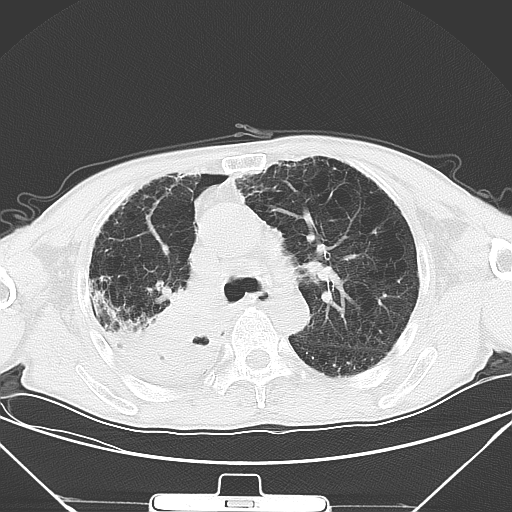
Chest CT, one axial slice; position 32 of 50 along the scan axis; 120 kVp; lung window (W 1500 / L -600 HU); 5 mm slice thickness; 512 × 512 image matrix, field of view 373 × 373 mm. Patient: male, 65 years. Case-level facts recorded for this patient, not image findings: clinical TNM (as recorded): T3 N1 M1a.
Structures marked on this image (rectangle marked by the reading radiologist):
- lung tumour (recorded histology: squamous cell carcinoma): bounding box (x1, y1, x2, y2) in pixels: (135, 279, 225, 369)